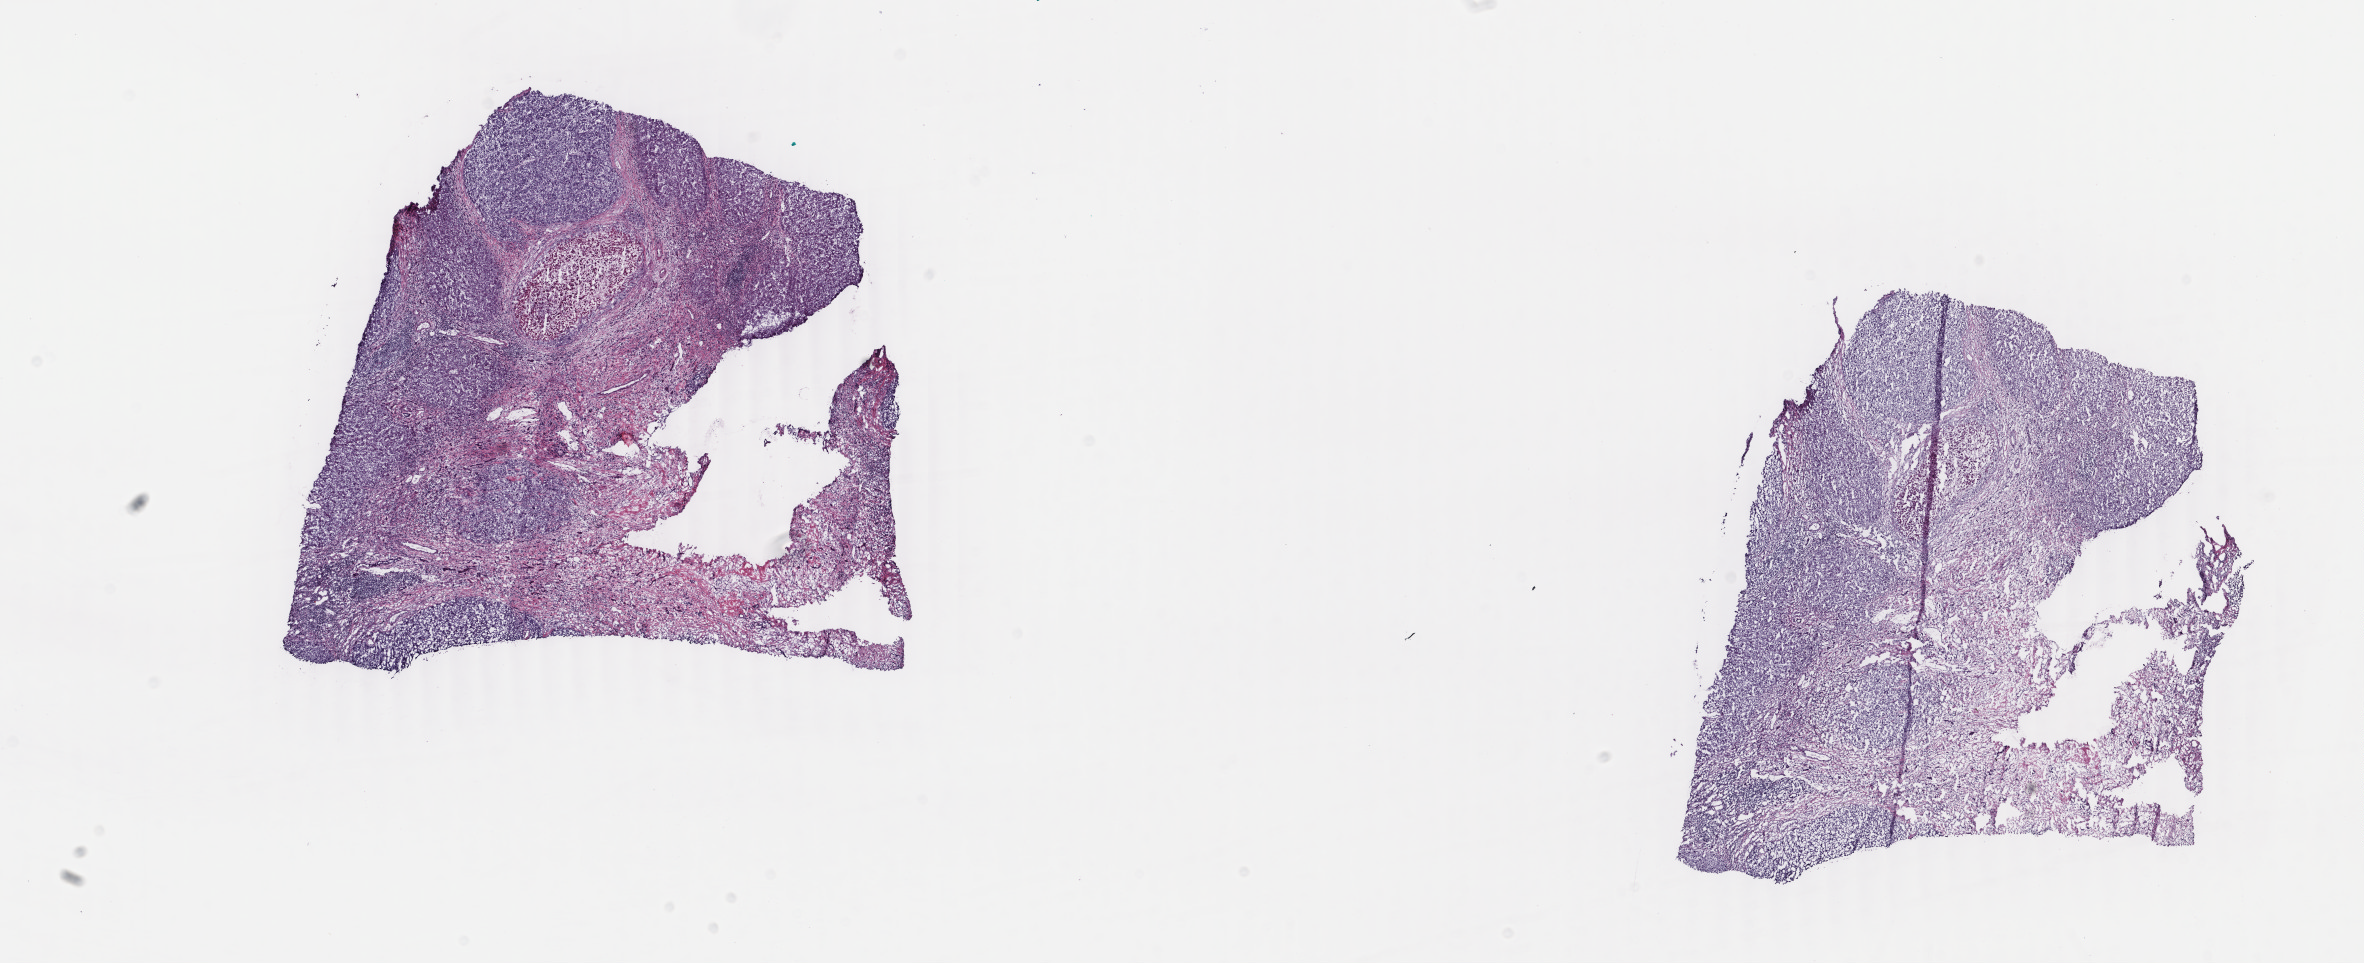
Whole-slide histology image, H&E-stained, shown as a low-resolution overview of the whole scanned area (about 18.8 x 7.7 mm, acquisition: 40x scan). Frozen section from the top of the tissue portion. Primary tumour sample from the liver. Patient: male, age at initial diagnosis 42 years. Histologic grade: G3 (poorly differentiated). Composition of this section per pathologist review: tumour cells 70%, tumour nuclei 70%, normal cells 5%, stromal cells 20%, necrosis 5%. Inflammatory infiltration, as recorded: lymphocyte infiltration 2%, monocyte infiltration 1%, neutrophil infiltration 2%.
AJCC pathologic stage: II (6th edition). Diagnosis: Hepatocellular carcinoma, NOS.